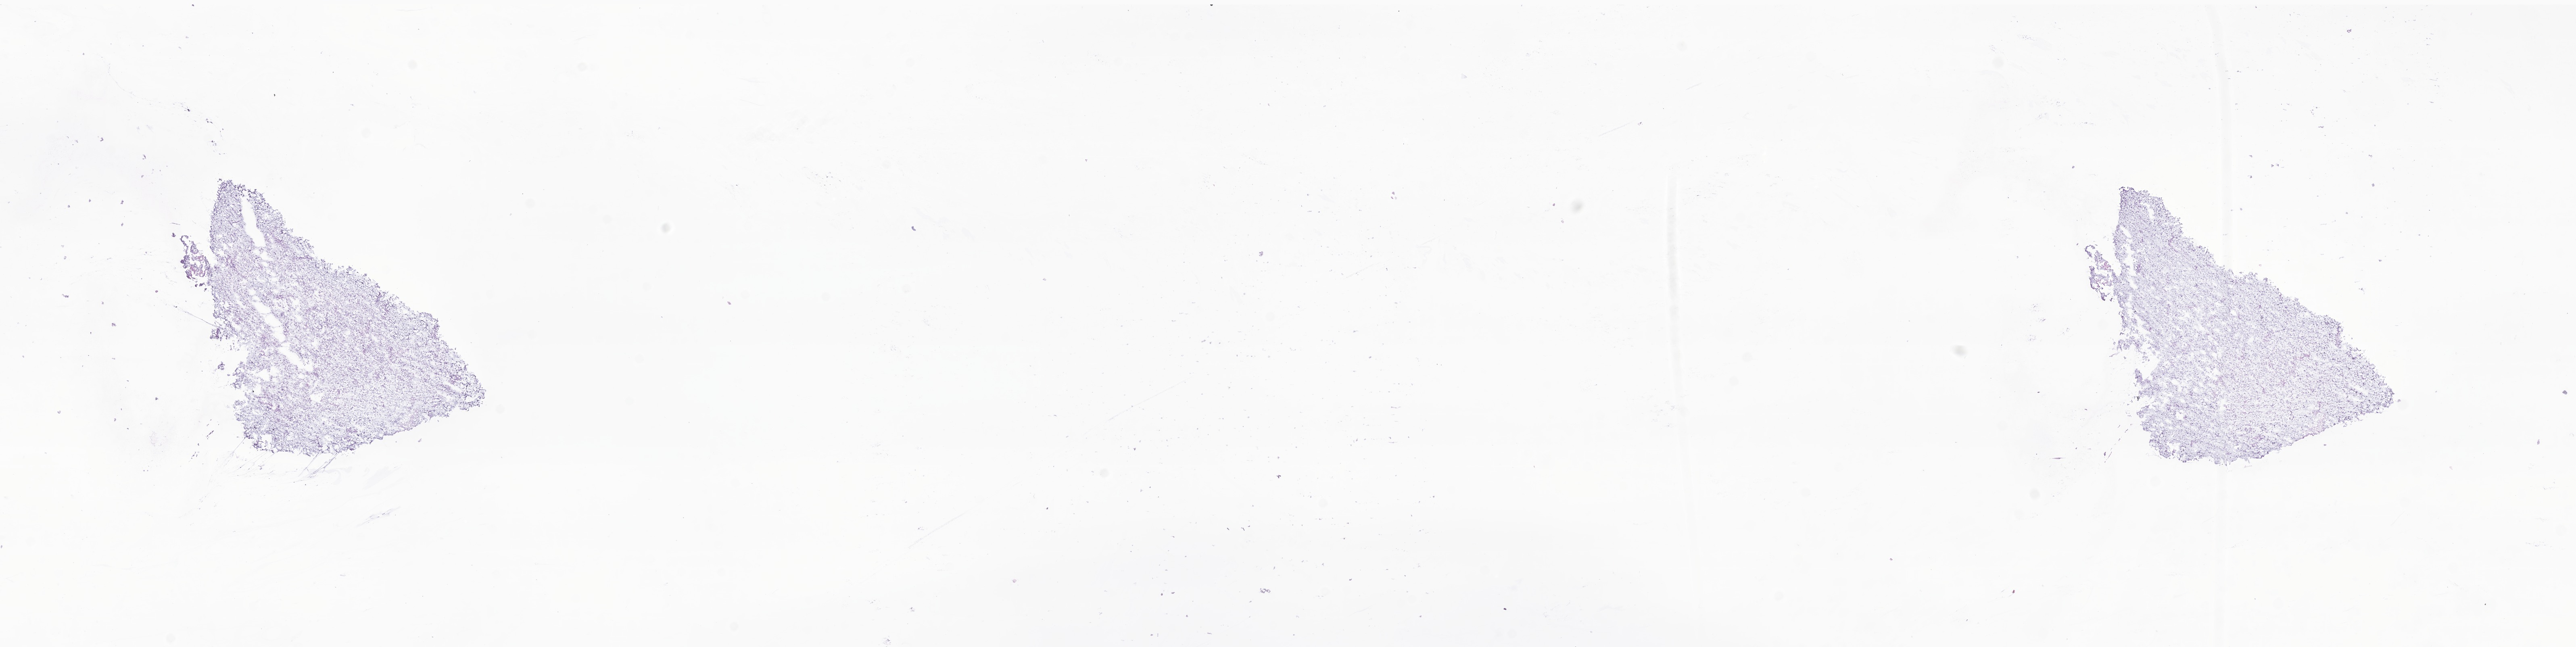
Haematoxylin and eosin whole-slide image of tumor tissue from the brain, low-resolution overview of the scanned area, about 26.9 x 6.8 mm, frozen section (OCT-embedded). Patient female; age 92 days.
Diagnosis (ICD-O-3 morphology term): Glioblastoma, NOS.